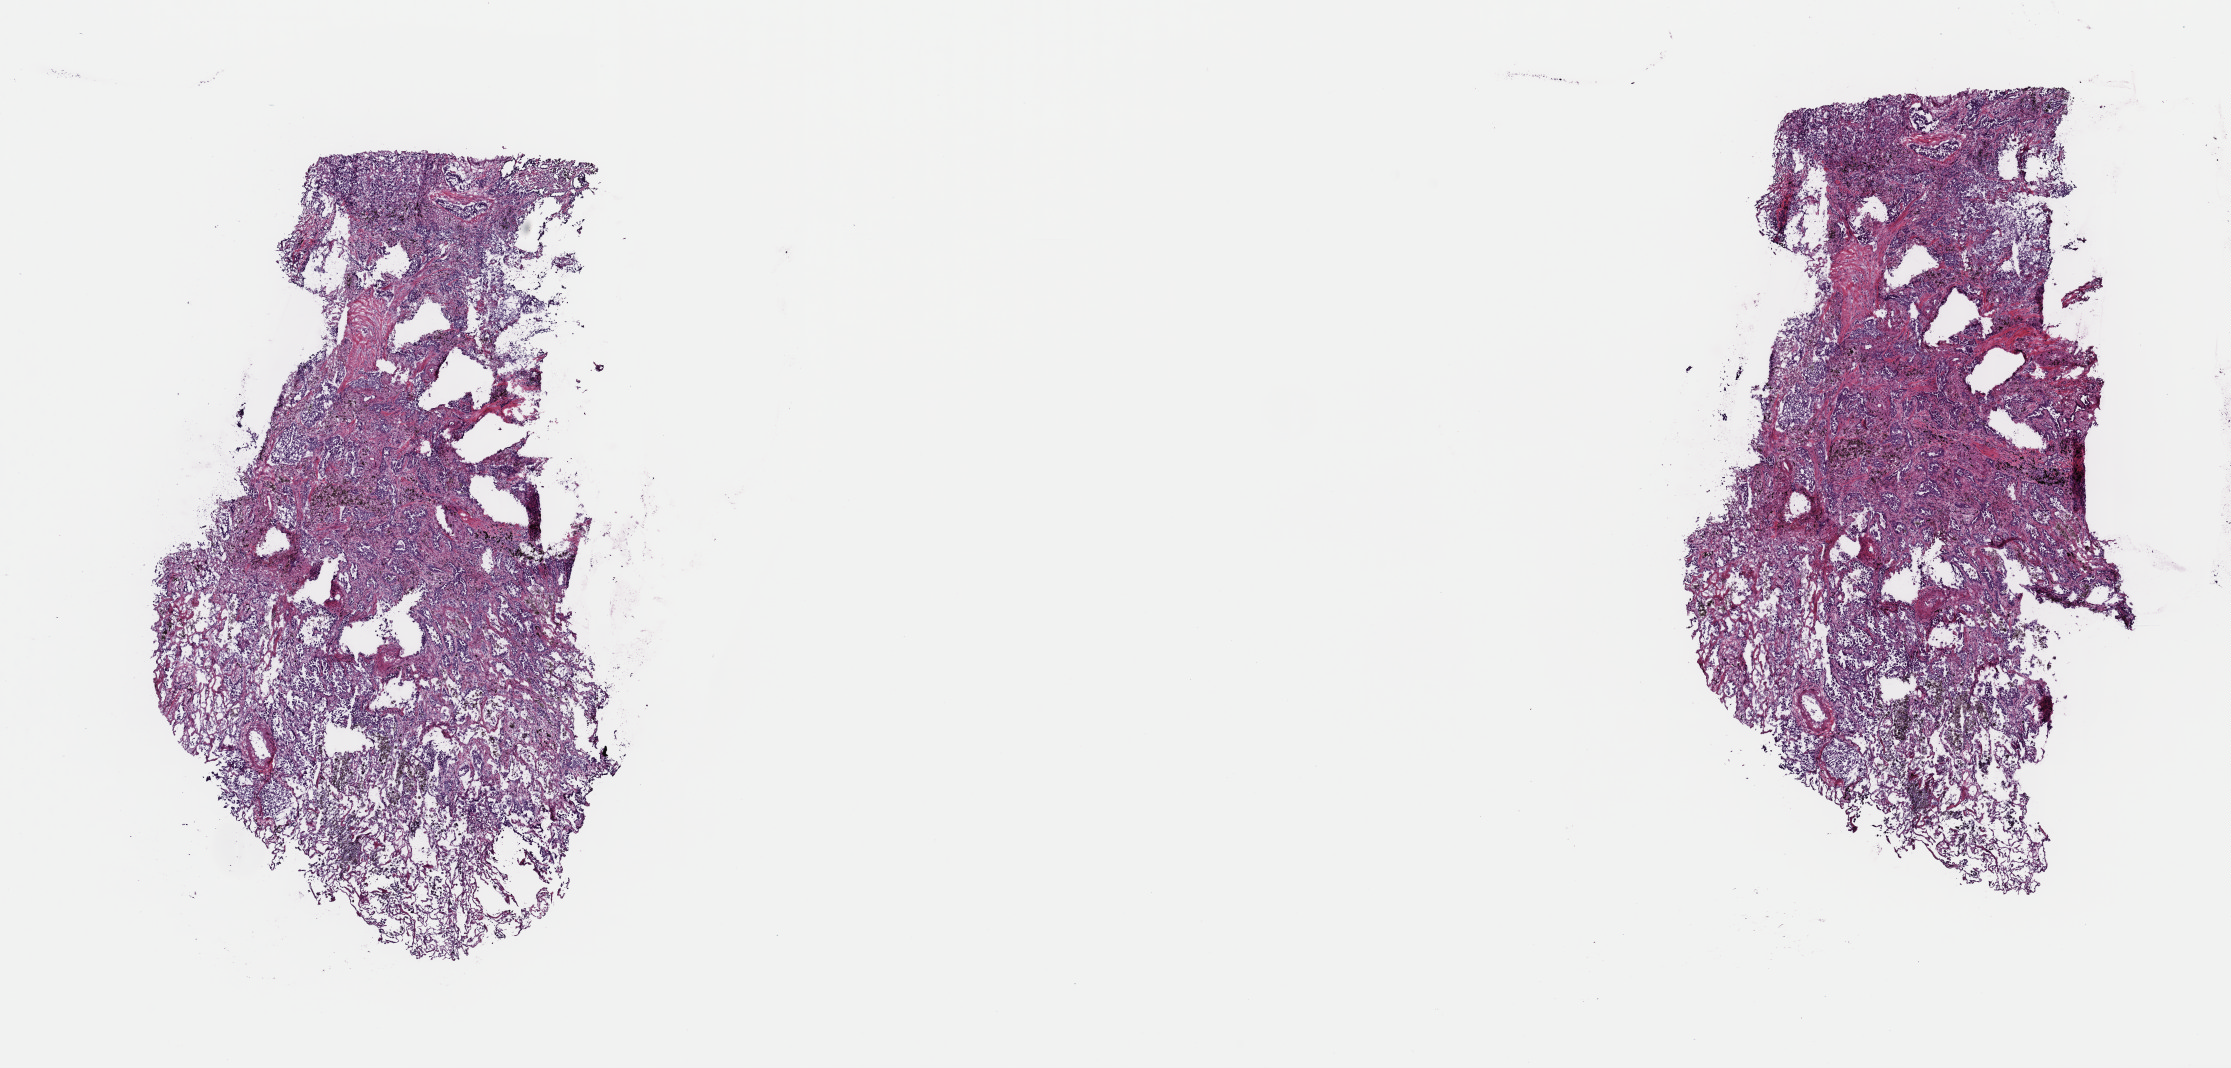
Whole-slide histology image, H&E-stained, whole scanned area (about 17.6 x 8.4 mm) shown as a low-resolution overview; frozen section from the top of the tissue portion; lung, primary tumour sample. Female patient; age at initial diagnosis 61 years. Pathologist review of this section (percent, as recorded): tumour cells 70%, tumour nuclei 70%, normal cells 10%, stromal cells 20%, necrosis 0%. Inflammatory infiltration, as recorded: lymphocyte infiltration 5%, monocyte infiltration 3%, neutrophil infiltration 0%.
AJCC pathologic stage: IA (7th edition). Histologic diagnosis: Adenocarcinoma, NOS (upper lobe, lung).